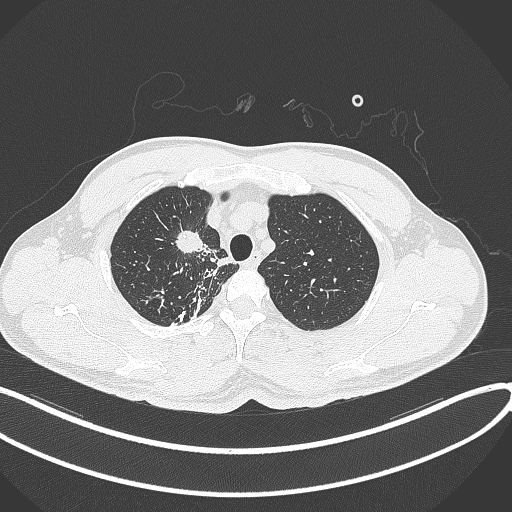
Chest CT, one axial slice; position 310 of 391 along the scan axis; 120 kVp; lung window (W 1500 / L -600 HU); 1 mm slice thickness; 512 × 512 image matrix, field of view 400 × 400 mm. Patient: male, 48 years. Case-level facts recorded for this patient, not image findings: clinical TNM (as recorded): T1c N1 M1.
Outlined on this slice (rectangle marked by the reading radiologist):
- lung tumour (recorded histology: adenocarcinoma): bounding box <171,223,208,258> (left, top, right, bottom; pixels)